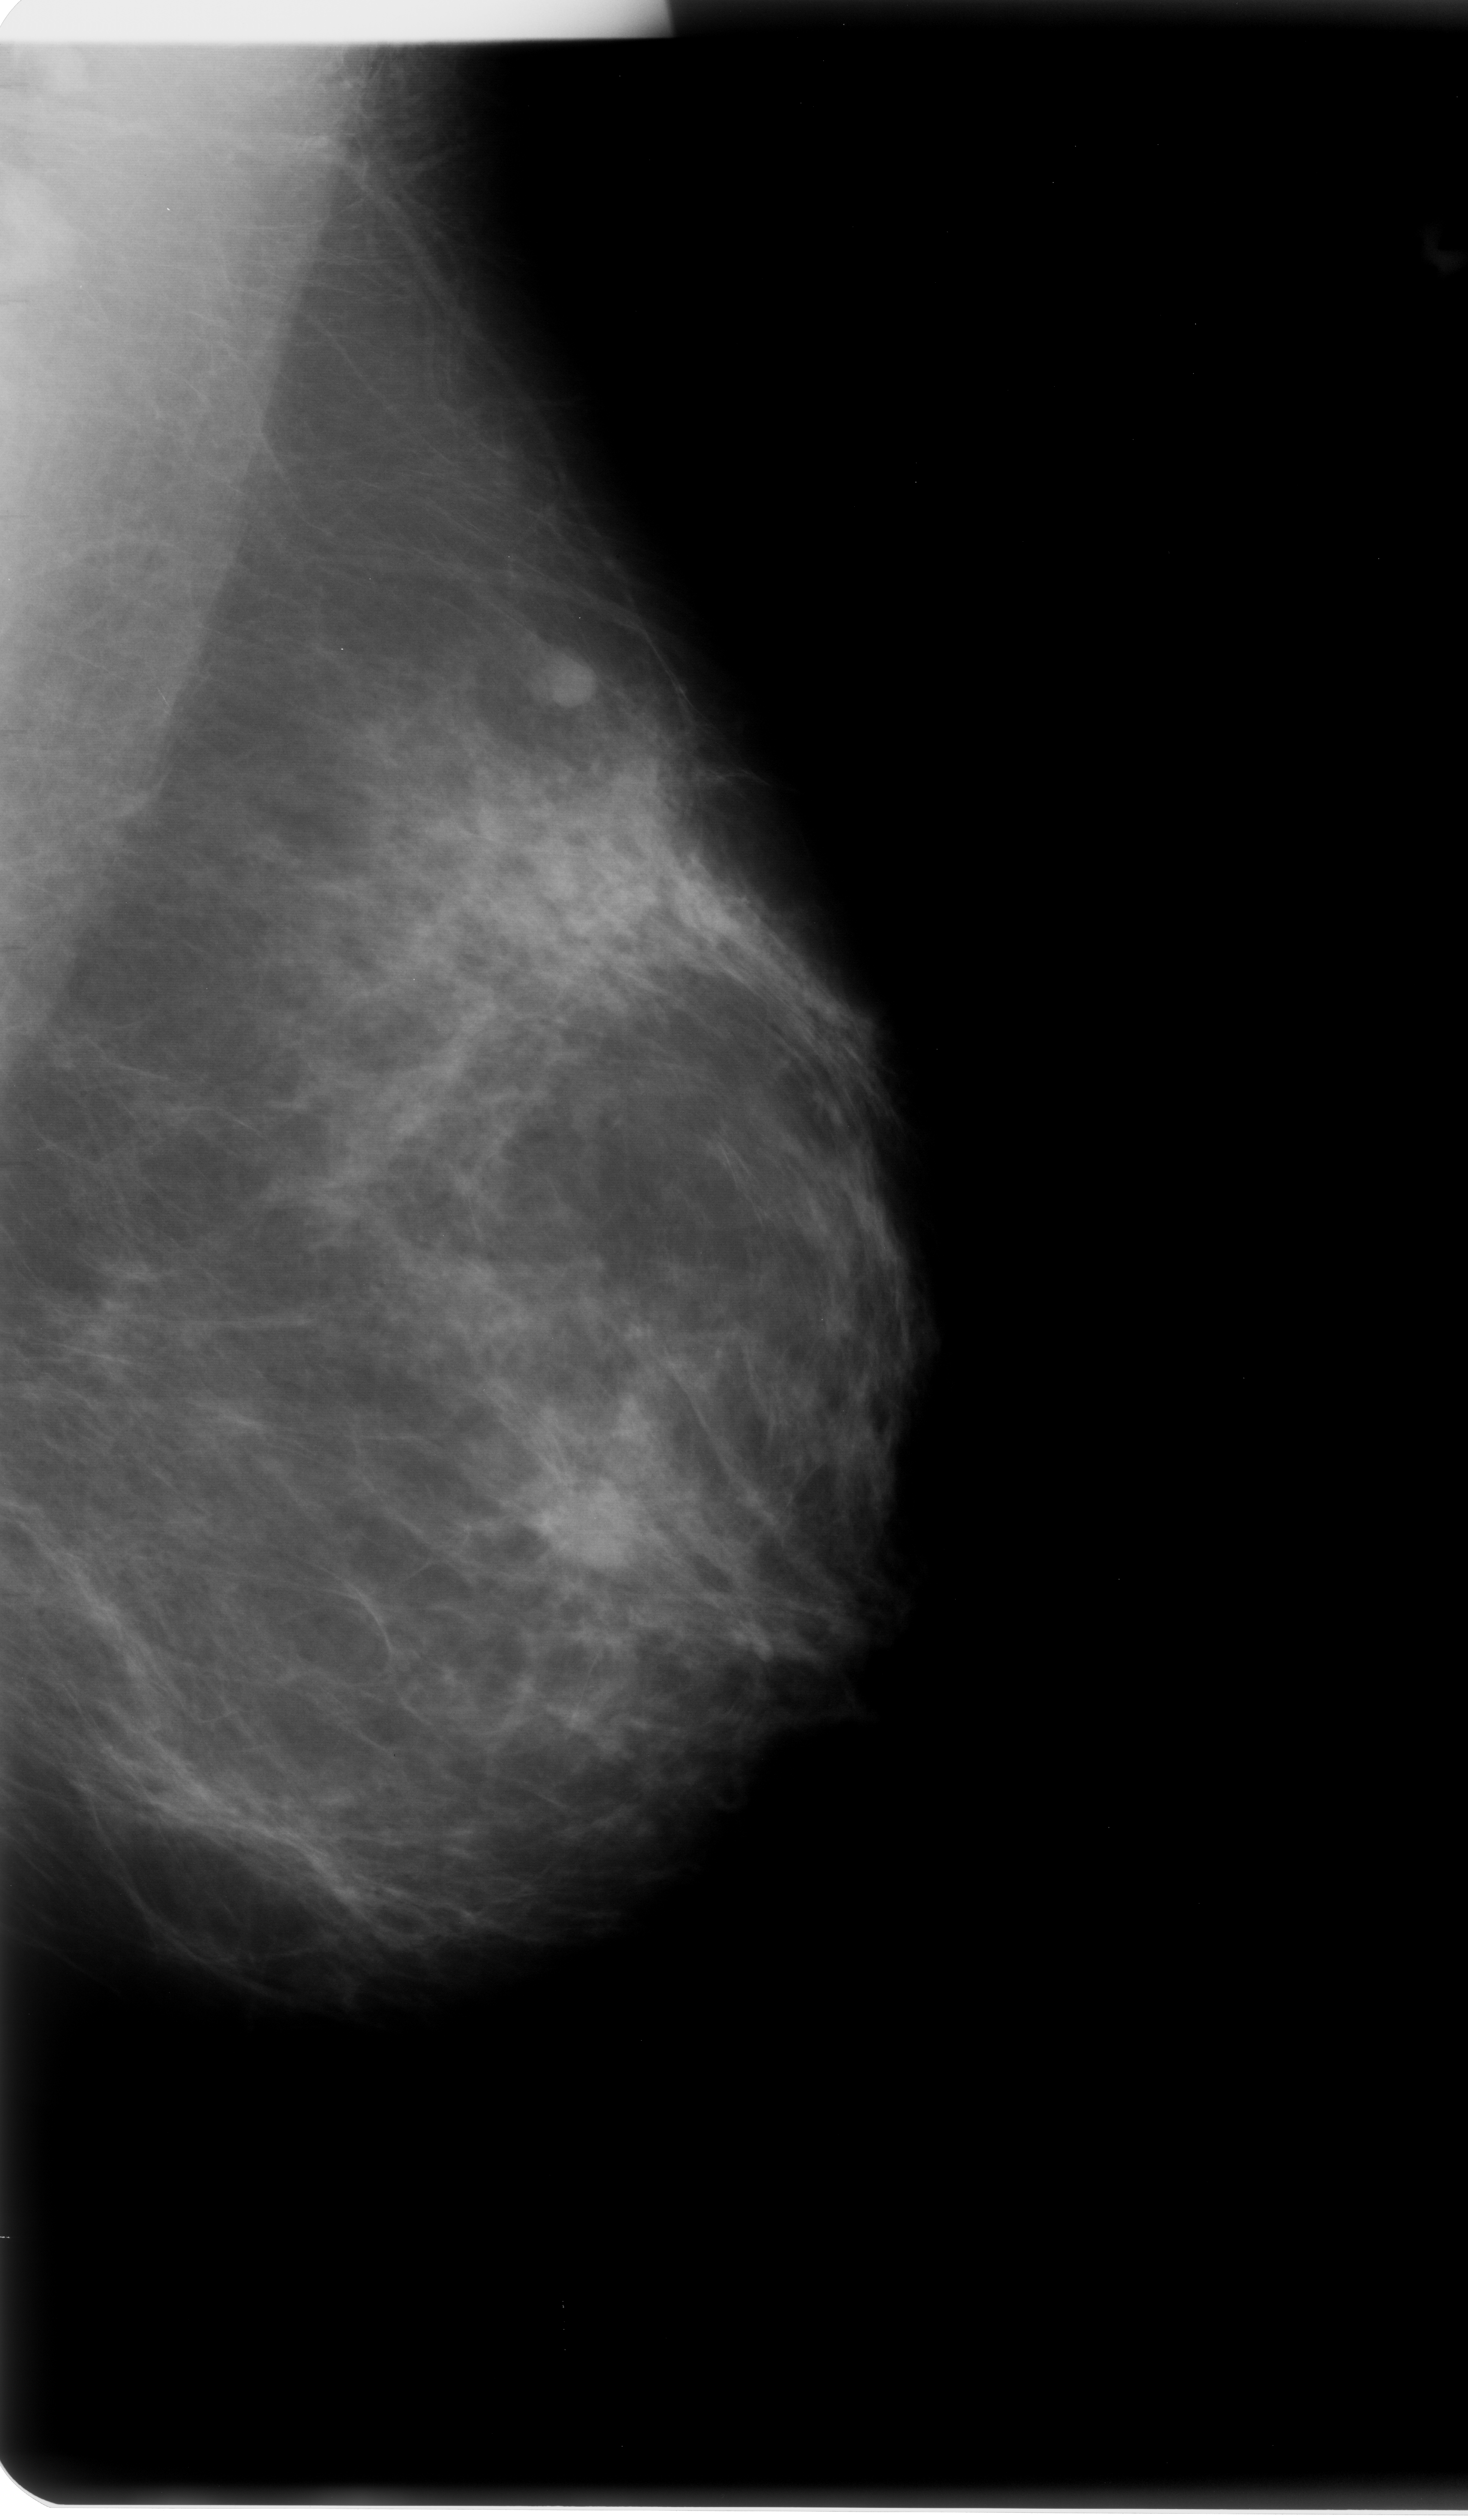
Mammogram (digitized film). Left breast. Mediolateral oblique (MLO) view. Breast composition: scattered fibroglandular densities (BI-RADS density category 2 of 4). 1468 × 2520 image matrix.
Marked abnormalities (boxes around the expert regions of interest):
- mass, shape round, margins spiculated; BI-RADS assessment category 5; pathology (as recorded): malignant: bounding box (x1, y1, x2, y2) in pixels: (510, 1452, 660, 1578)